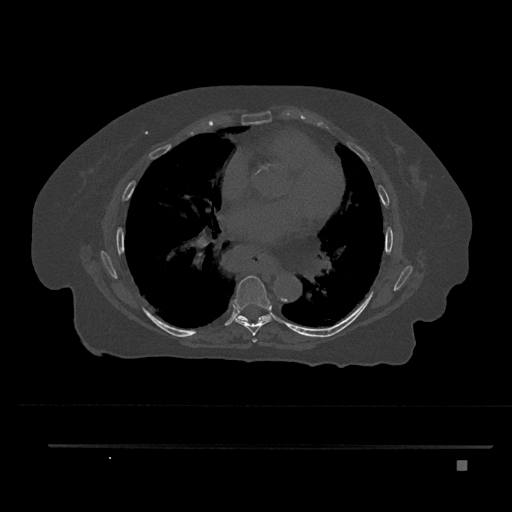
CT including the spine, one axial slice; position 474 of 797 along the scan axis; reconstruction kernel Br40s/3; 120 kVp; bone window (W 1800 / L 400 HU); 0.5 mm slice thickness; 512 × 512 image matrix. Female patient, age 76 years. Case-level facts recorded for this patient, not image findings: primary cancer: lung.
Structures marked on this image (semi-automatically segmented with operator editing):
- T6 vertebra: bounding box <252,338,257,343> (left, top, right, bottom; pixels)
- T7 vertebra: <234,275,272,336>
- T8 vertebra: <236,314,270,321>